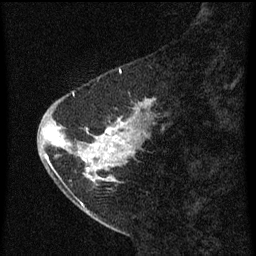
Breast MRI (dynamic contrast-enhanced), one sagittal slice. Position 19 of 60 along the scan axis. Dynamic contrast-enhanced series, image 2 of 3 at this slice position (ordered by acquisition). 1.5 T. TE 4.2 ms, TR 8 ms. 2 mm slice thickness. 256 × 256 image matrix, field of view 180 × 180 mm. Female patient, age 47 years.
Outlined on this slice (semi-automatic segmentation, software-assisted and operator-edited):
- analysis volume of interest (the breast-tissue region the enhancement analysis was run in; not a lesion): bounding box [x1, y1, x2, y2] px = [44, 84, 155, 199]
- tumour enhancement mask (voxels above the 70 % enhancement threshold inside the analysis volume of interest): [46, 94, 147, 181]